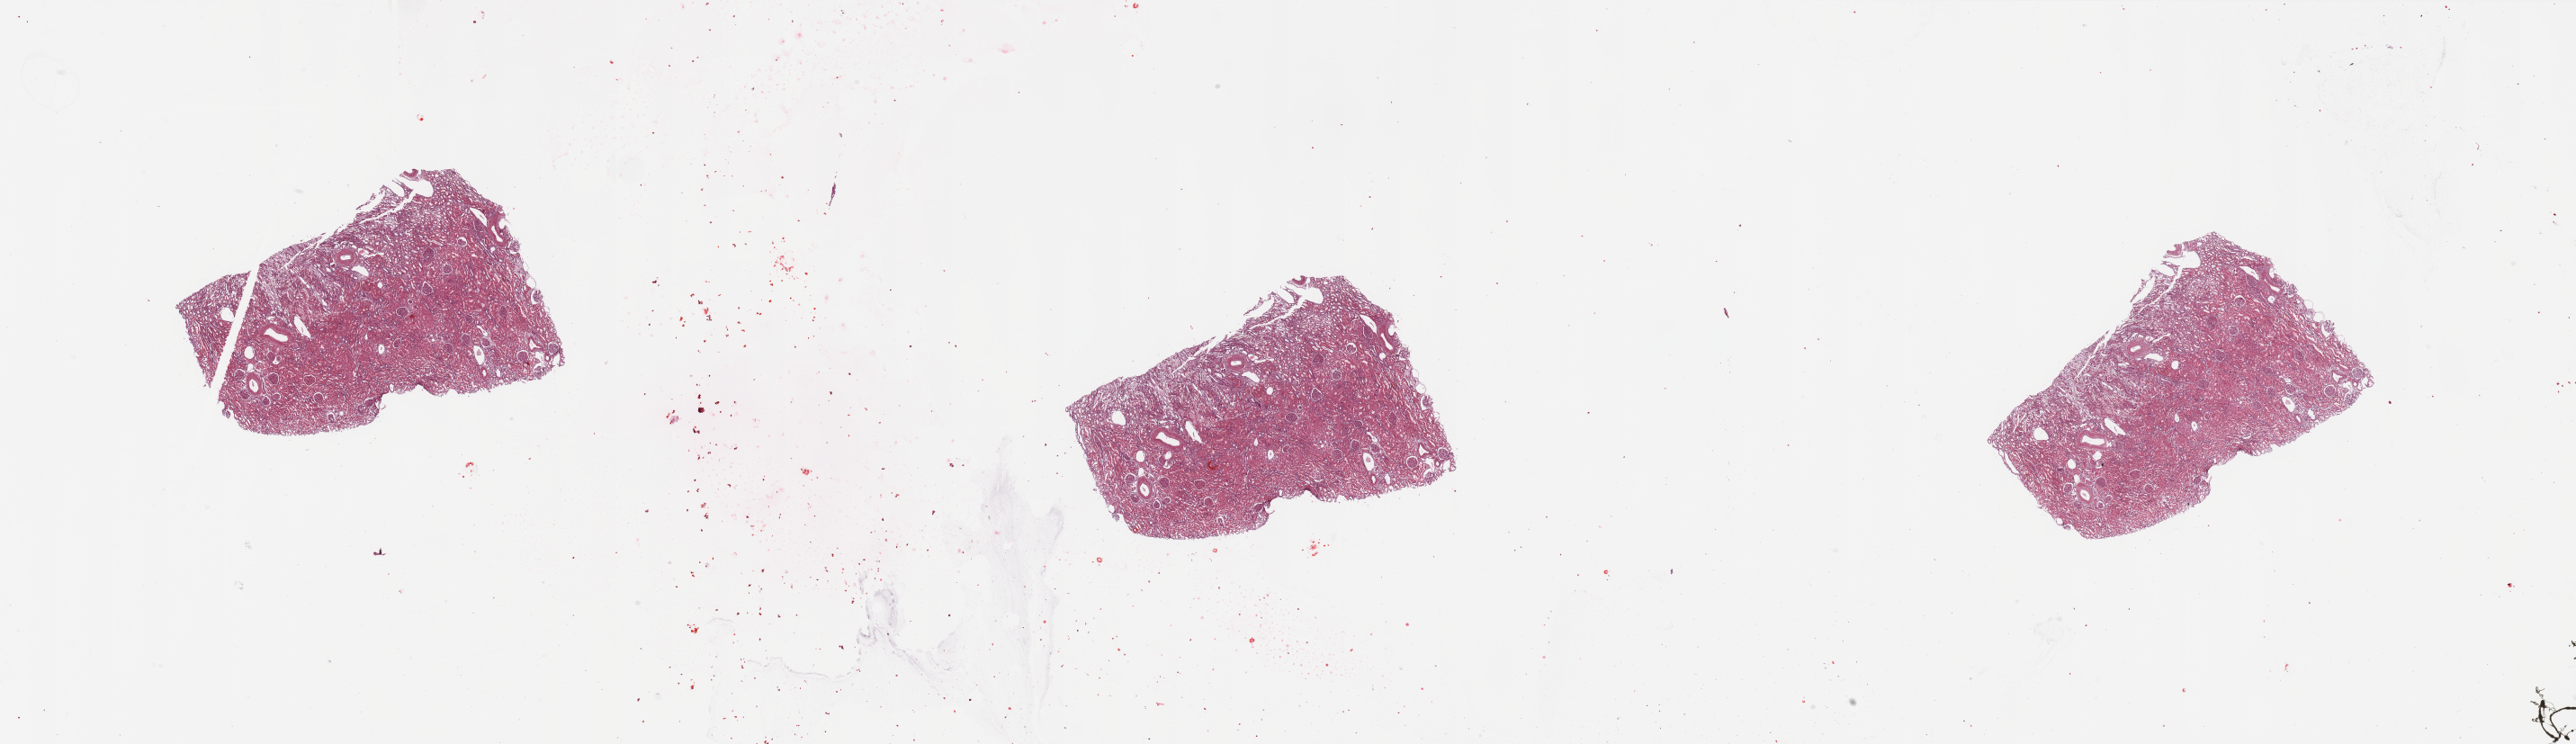
H&E whole-slide image — a low-resolution overview of the entire scanned area, about 45.3 x 13.1 mm (from a 20x scan), normal (non-tumour) tissue sample, sampled site: kidney. 72-year-old male patient.
* this section: normal (non-tumour) tissue from the same patient
* patient diagnosis: Renal cell carcinoma, NOS